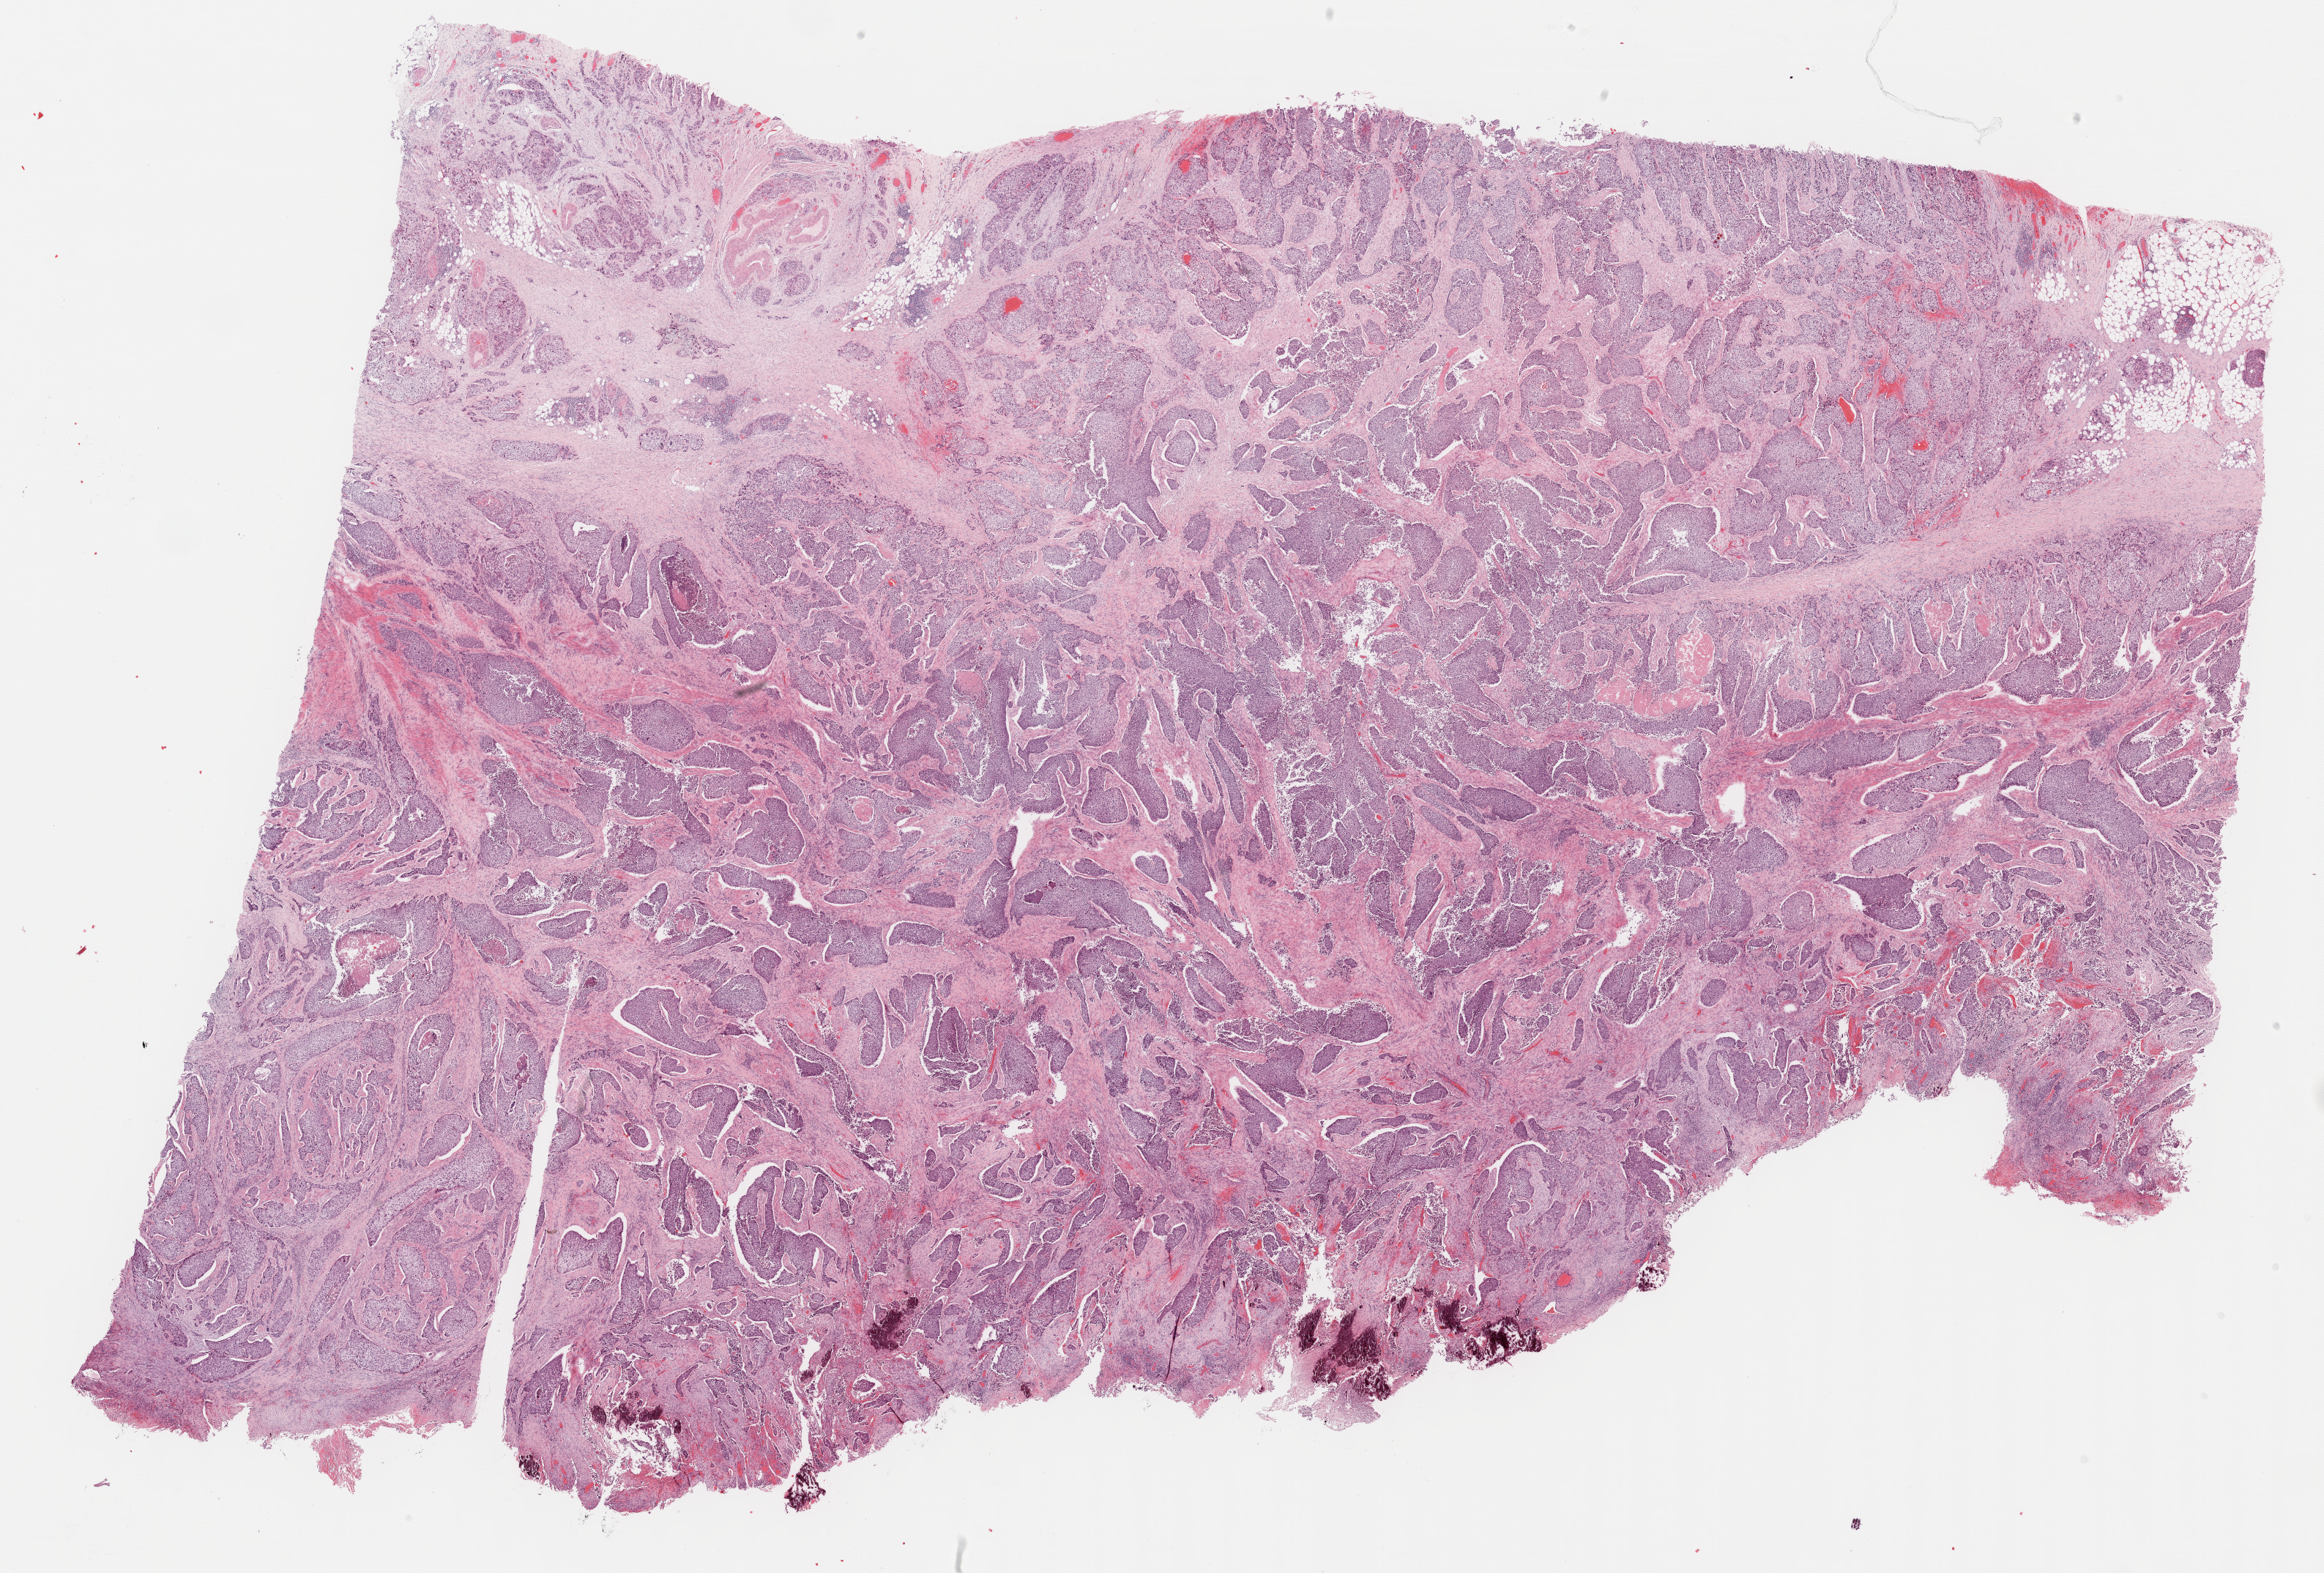
Digitized Hematoxylin and eosin (H&E) stained tissue section (whole slide) — low-resolution overview of the scanned area, about 25.7 x 17.4 mm (from a 40x scan); formalin-fixed paraffin-embedded (FFPE) diagnostic section; bladder, primary tumour sample. Male, age 58 years at initial diagnosis. Histologic grade: high grade.
Lymph nodes positive (case pathology): 1 of 1 examined. Diagnosis: Transitional cell carcinoma. AJCC pathologic stage: IV (7th edition).